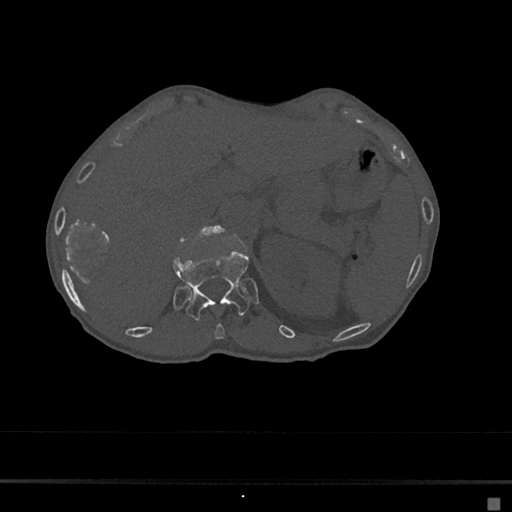
CT including the spine, one axial slice. Position 126 of 797 along the scan axis. 120 kVp. Bone window (W 1800 / L 400 HU). 0.5 mm slice thickness. 512 × 512 image matrix, field of view 360 × 360 mm. Patient: female, 68 years. From the clinical record (not read from this slice): primary cancer: renal.
Annotated regions visible in this slice (semi-automatically segmented with operator editing):
- L1 vertebra: box from (x=198, y=228) to (x=221, y=236) px
- T11 vertebra: (x=214, y=323)–(x=225, y=340)
- T12 vertebra: (x=173, y=250)–(x=249, y=321)